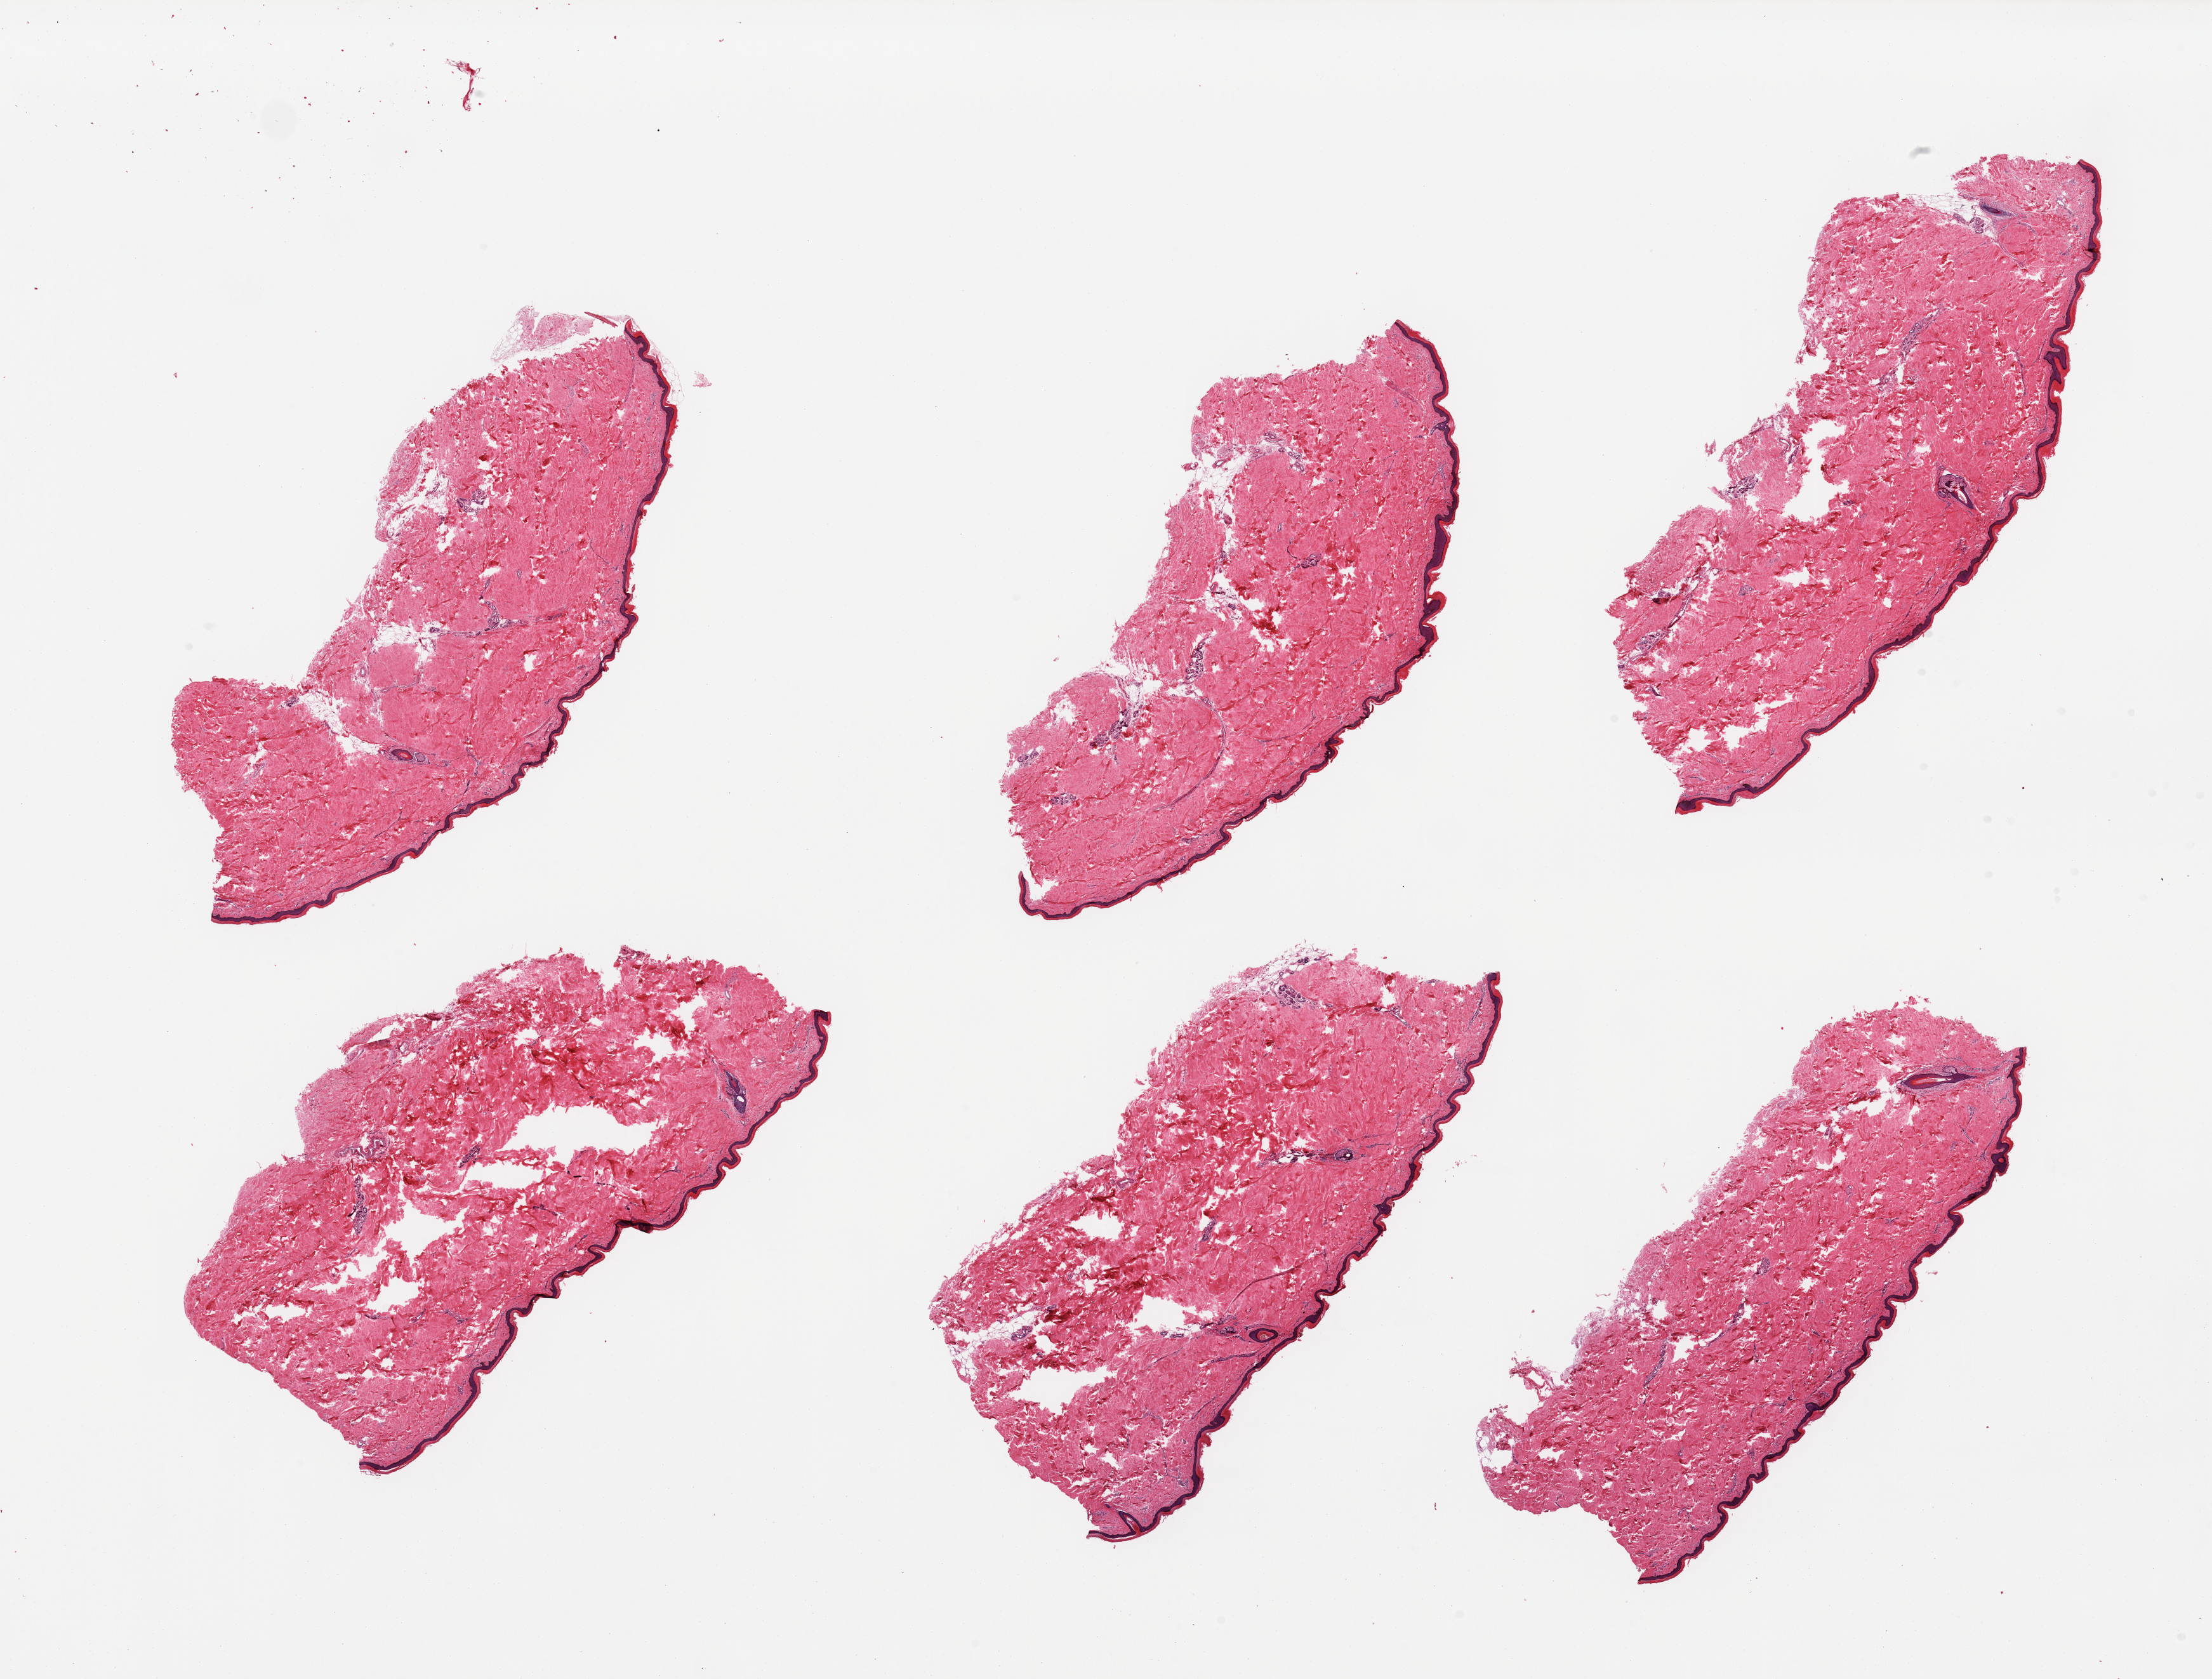
Whole-slide image, hematoxylin and eosin (H&E) stain, shown as a low-resolution overview of the whole scanned area (about 27.6 x 20.9 mm), PAXgene-fixed, paraffin-embedded tissue, section of skin of lower leg (target tissue), tissue donor sample. Male donor.
Reviewer comment on this tissue sample: 6 pieces, no dermal fat; squamous epithelium is ~50 microns.